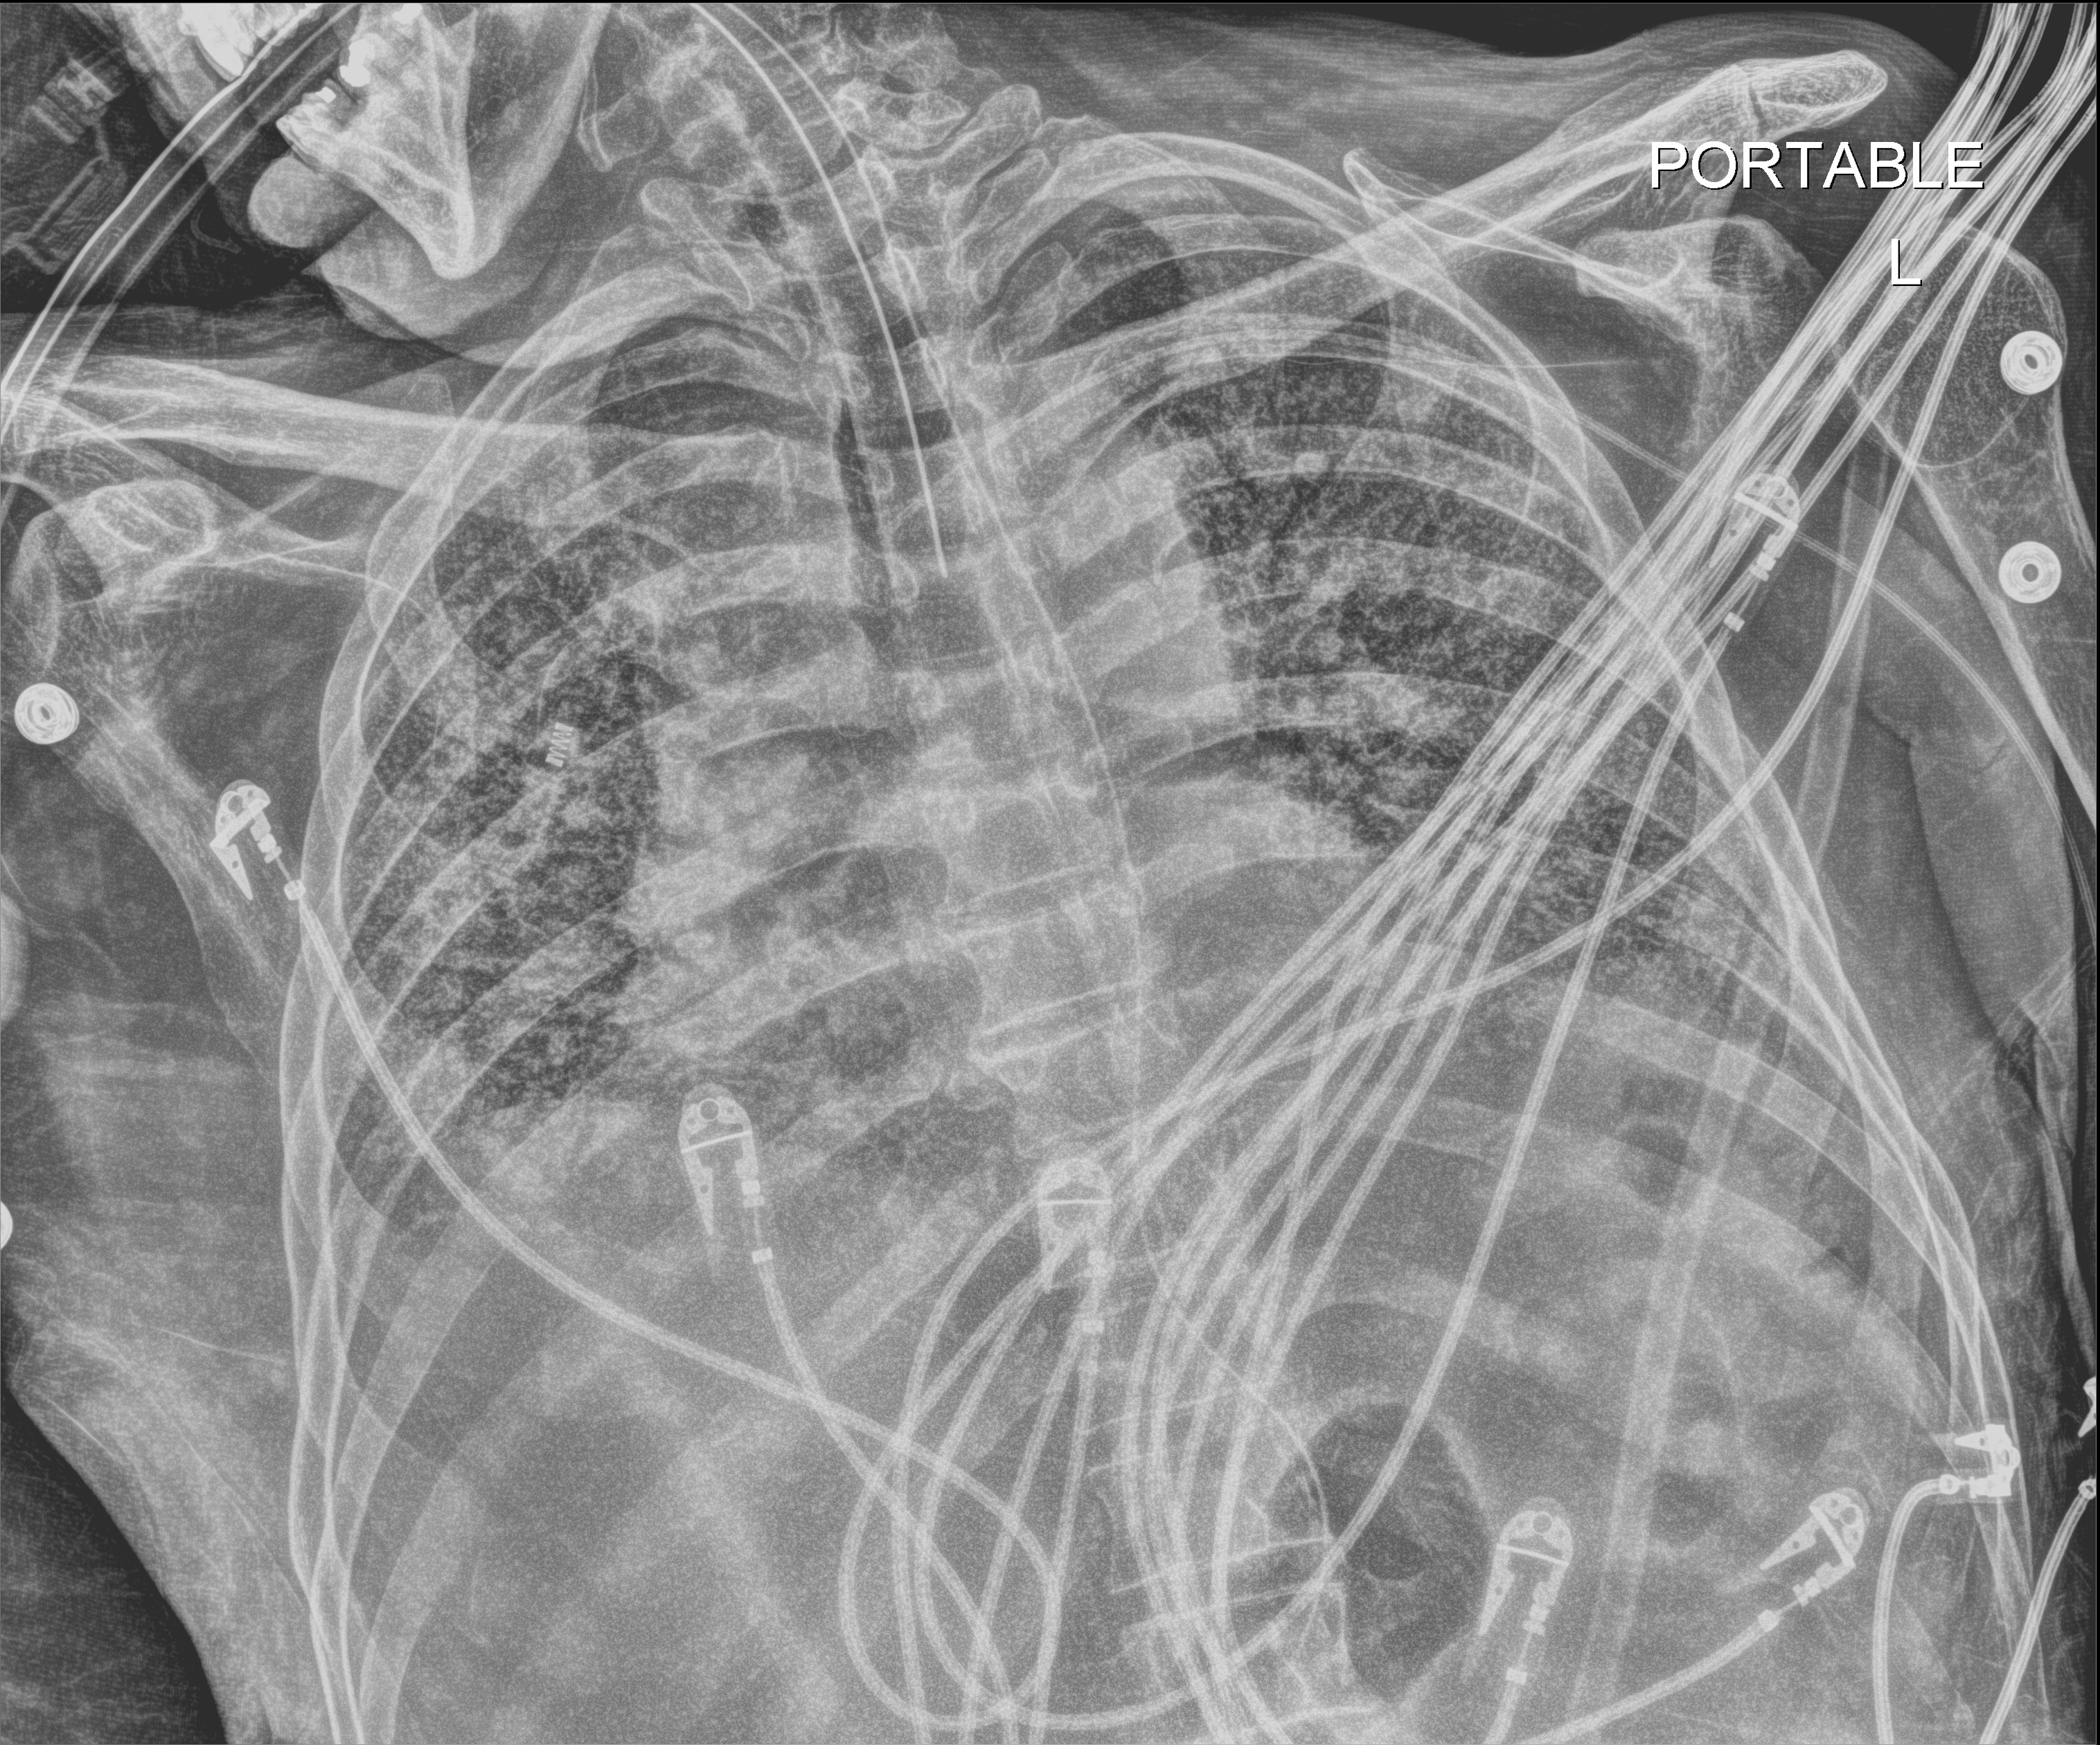
Chest X-ray, anteroposterior (AP) projection. Male patient hospitalised with COVID-19, age 60–74 years.
From the hospital-stay record, not from the radiograph (when in the stay this image was taken is not recorded):
- length of hospital stay: 54 days
- mechanically ventilated during this hospital stay: yes
- admitted to intensive care during this hospital stay: yes